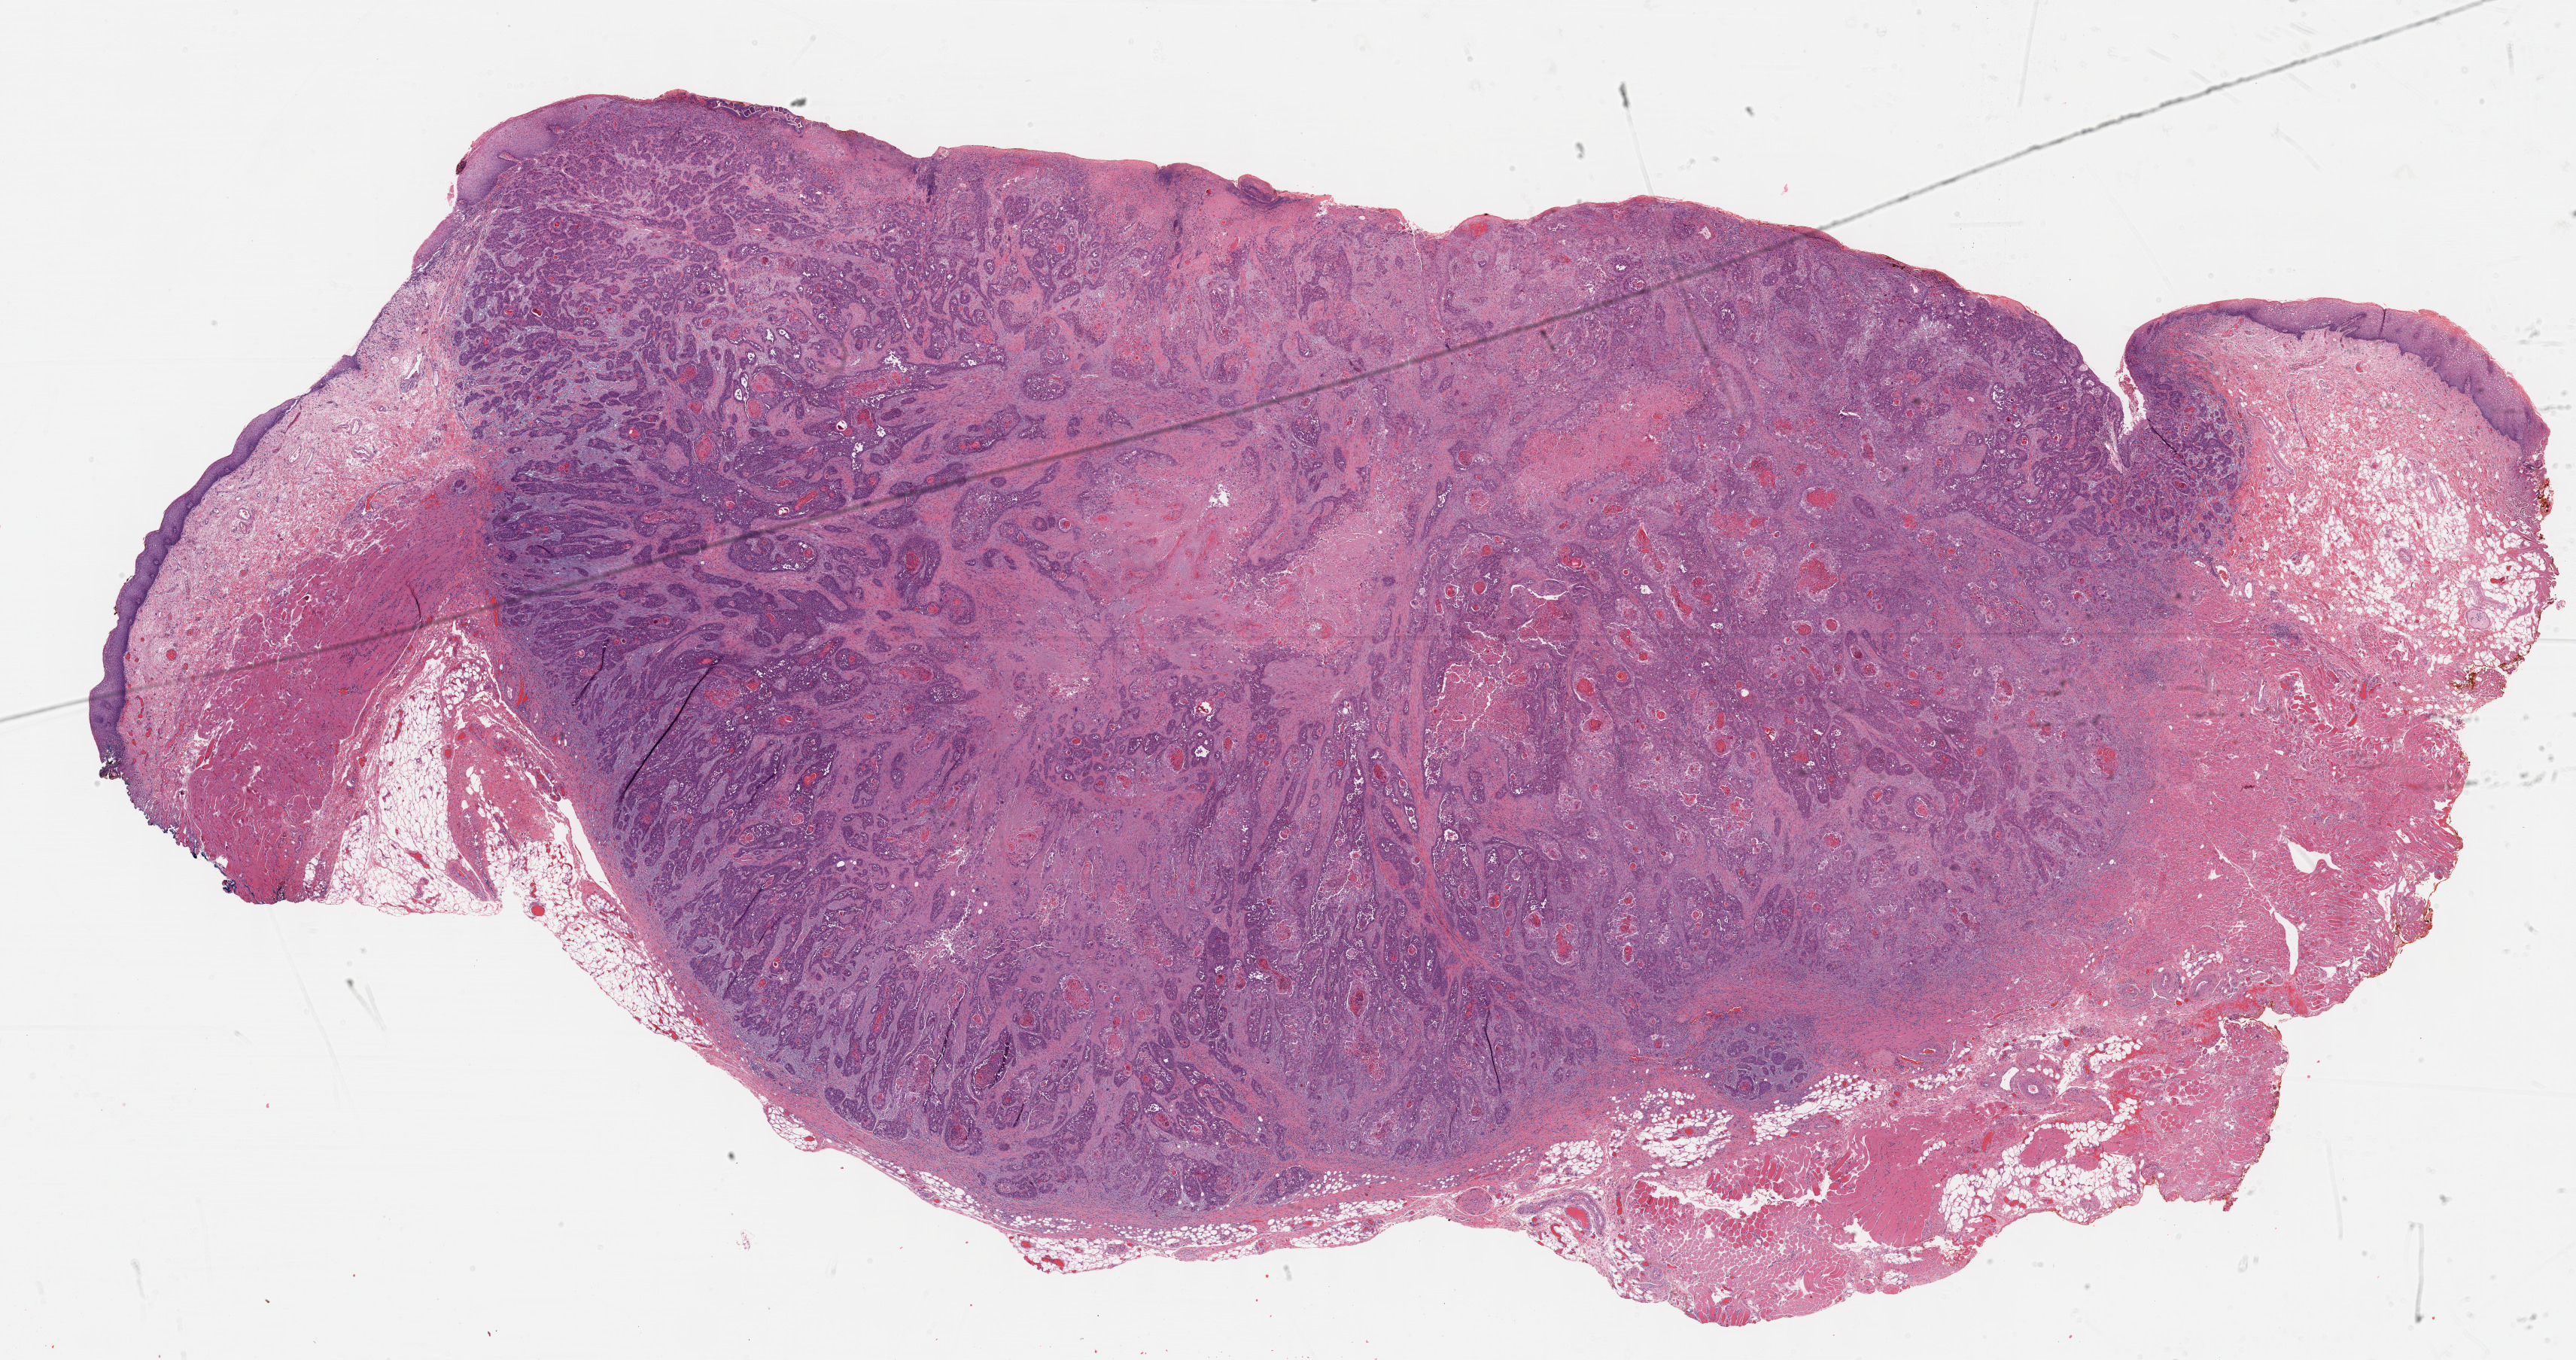
H&E-stained whole-slide image — shown as a low-resolution overview of the whole scanned area (about 27.7 x 14.6 mm); FFPE section; primary tumour sample from the head and neck. Patient: female, age at initial diagnosis 80 years.
Histologic diagnosis: Squamous cell carcinoma, NOS (cheek mucosa).